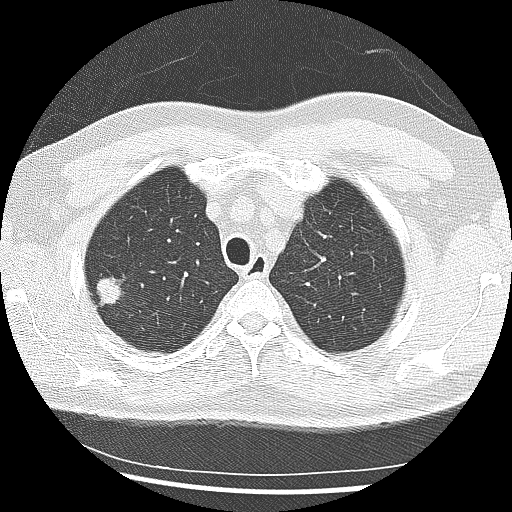
Low-dose screening chest CT, one axial slice; position 214 of 265 along the scan axis; reconstruction kernel LUNG; lung window (W 1500 / L -600 HU); 512 × 512 image matrix, field of view 340 × 340 mm.
Annotated regions visible in this slice (manually delineated by an expert):
- lesion 1 (tumor, upper lobe of right lung): bounding box [x1, y1, x2, y2] px = [97, 276, 121, 305]